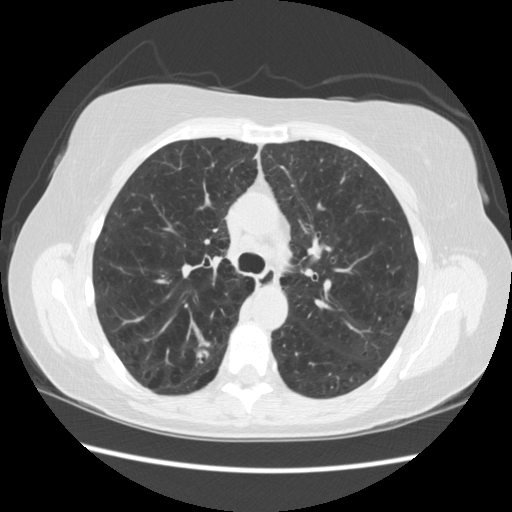
Chest CT (low-dose screening protocol), one axial image, third screening round (two years after baseline), lung window (W 1500 / L -600 HU), 2.5 mm slice thickness, standard (soft-tissue) reconstruction kernel (STANDARD), slice 80 of 235 in the series. Female, age 55 years at enrolment. Current smoker at enrolment.
Expert-annotated lung lesion, bounding box <174,325,228,376> (left, top, right, bottom; pixels). Reader record for this screening exam (exam-level; its link to the box is not recorded): non-calcified nodule or mass ≥4 mm, right upper lobe, 11 × 11 mm, poorly defined margins, soft tissue attenuation, pre-existing on the prior screen: no. Later outcome: lung cancer diagnosed 96 days after this screen — small cell carcinoma, NOS, right upper lobe.